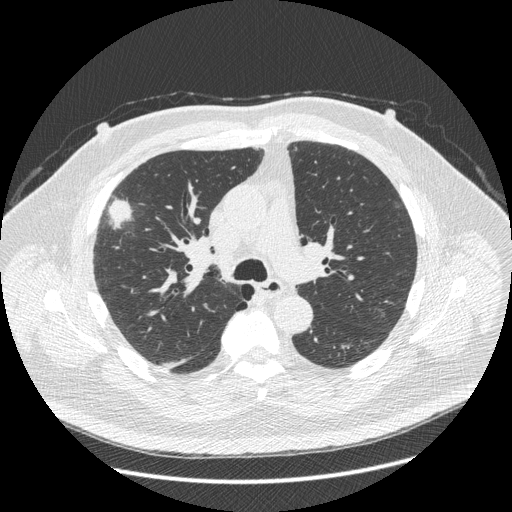
Low-dose screening chest CT, one axial slice. Position 275 of 426 along the scan axis. Reconstruction kernel STANDARD. Lung window (W 1500 / L -600 HU). 1.25 mm slice thickness. 512 × 512 image matrix, field of view 400 × 400 mm.
Annotated regions visible in this slice (expert manual segmentation):
- lesion 1 (tumor, upper lobe of right lung): bounding box (x1, y1, x2, y2) in pixels: (109, 200, 131, 227)